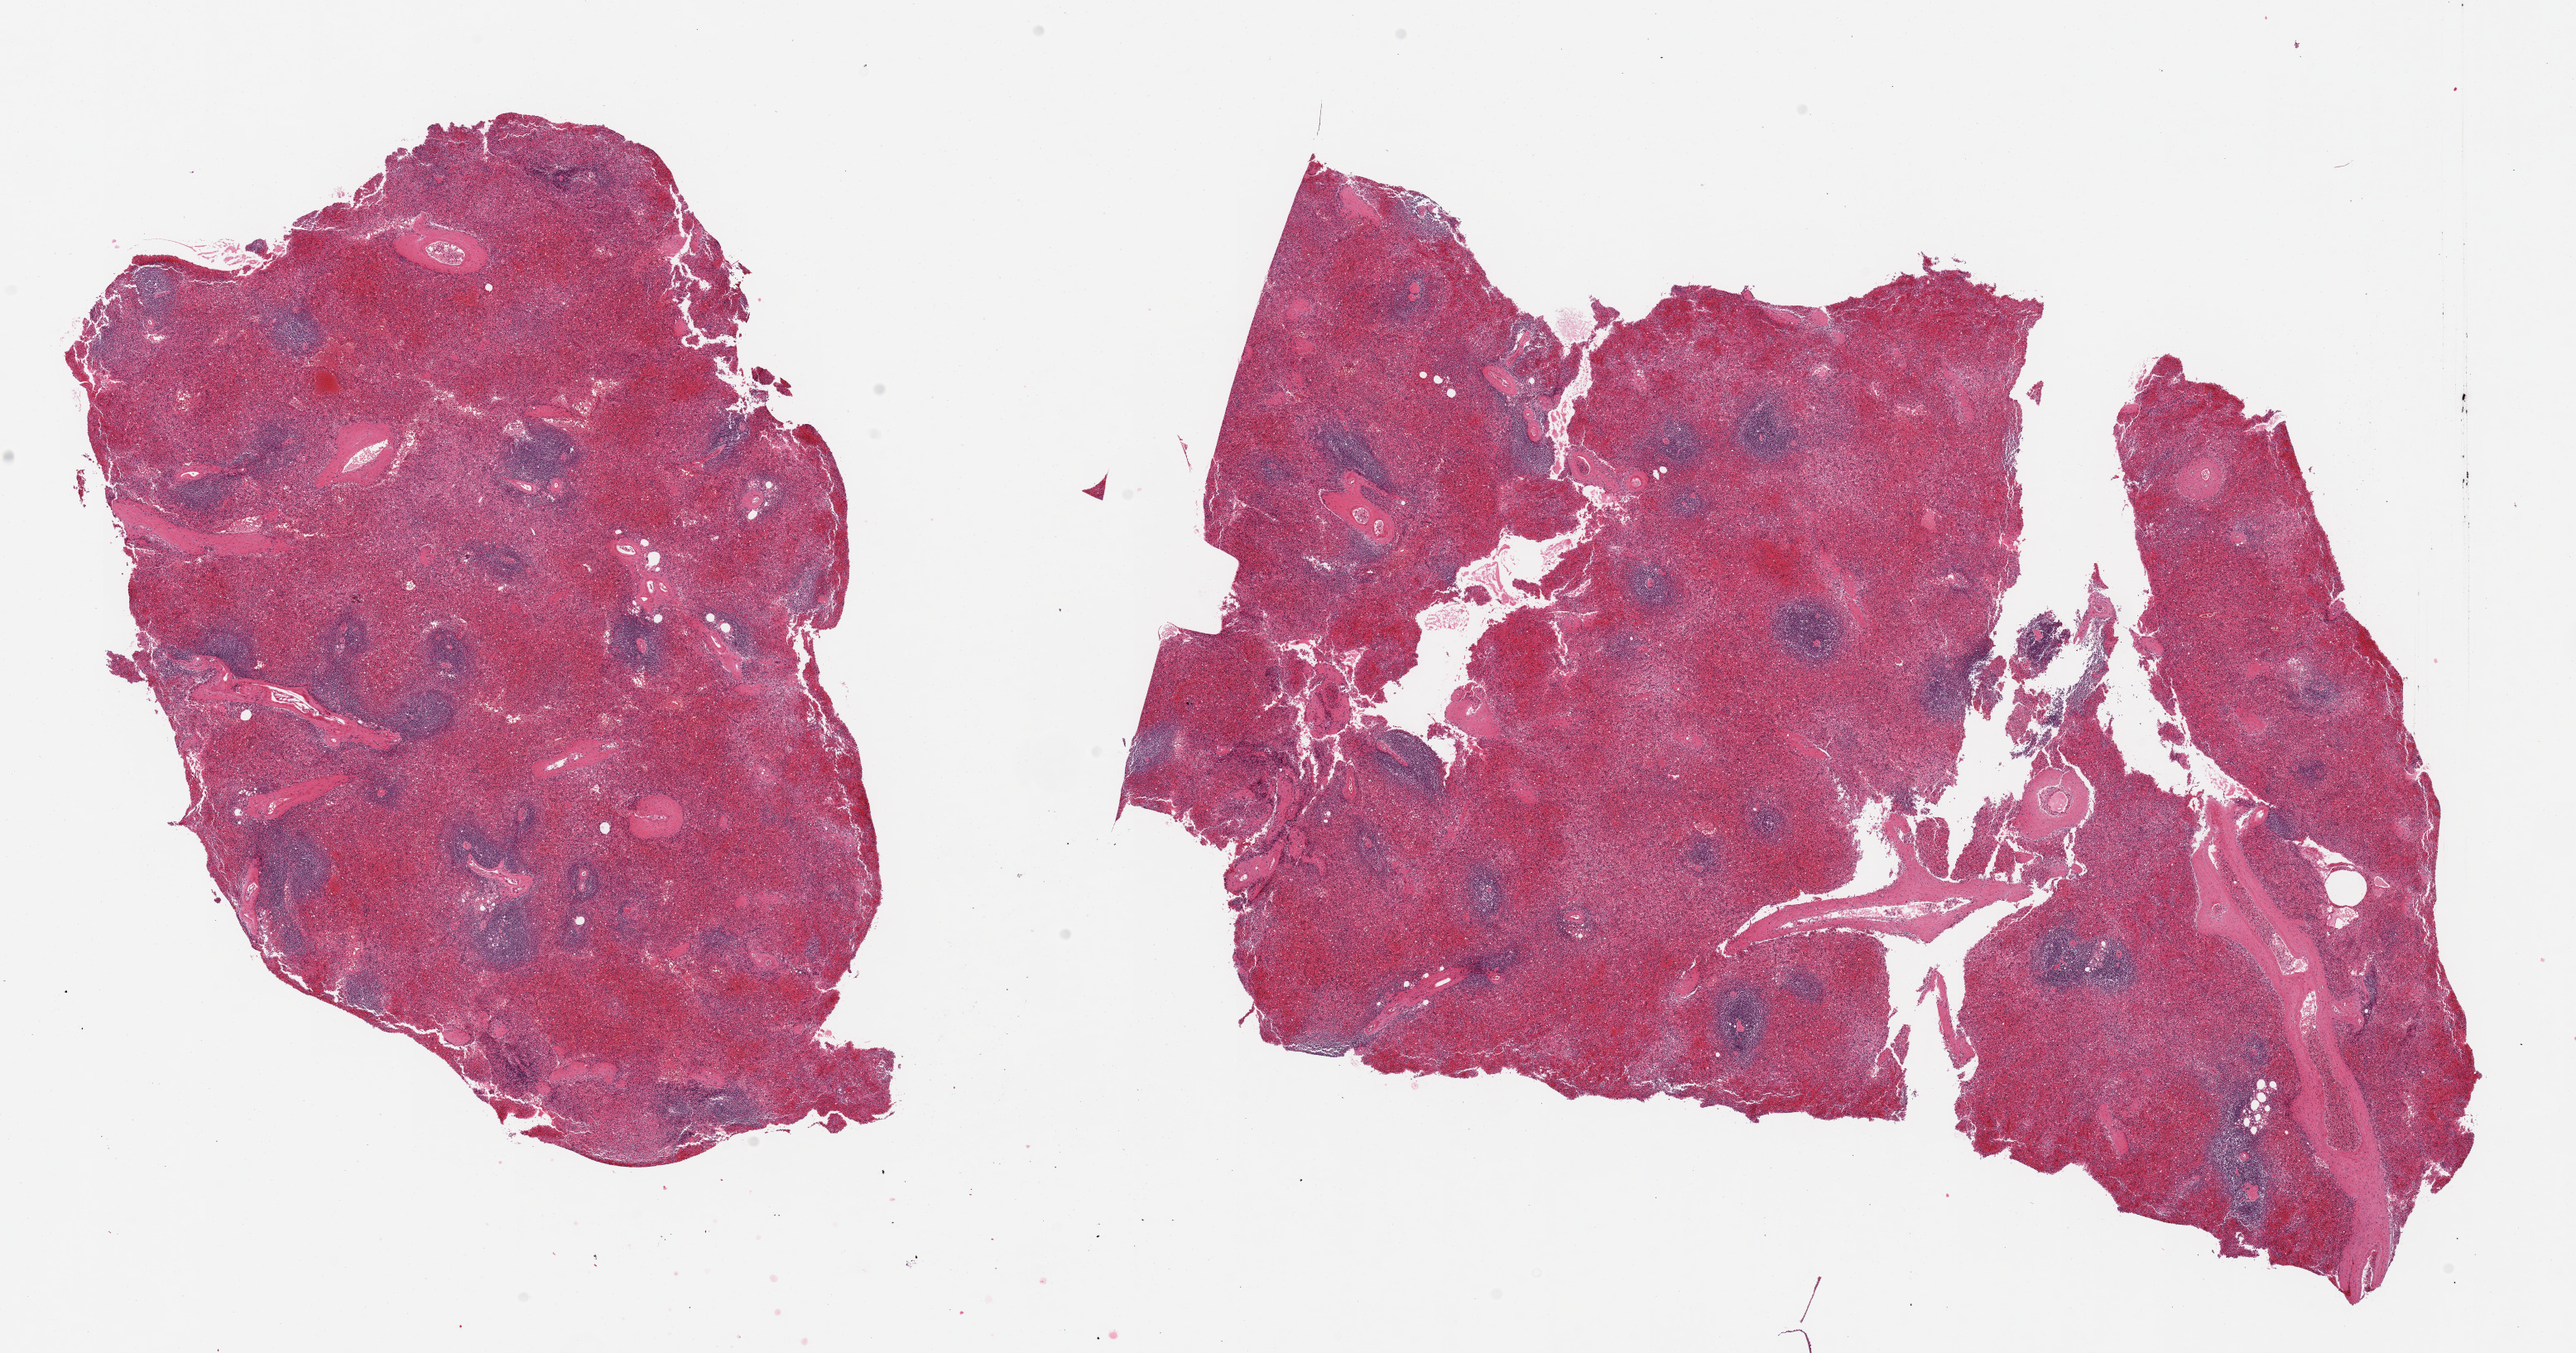
Hematoxylin and eosin (H&E) whole-slide image — shown as a low-resolution overview of the whole scanned area (about 24.6 x 12.9 mm, acquisition: 20x scan). PAXgene-fixed, paraffin-embedded tissue. Target tissue: spleen. Tissue donor sample.
Review note (as recorded): 2 pieces; congestion.